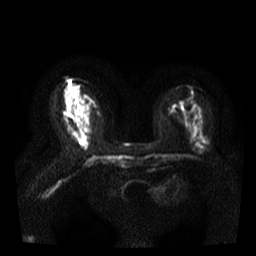
Breast MRI, one axial slice. Slice 18 of 40 in the series (ordered by position). Diffusion-weighted series; image 2 of 4 stored at this slice position (different b-values; order by instance number). 3 T. 5 mm slice thickness. 256 × 256 image matrix, field of view 300 × 300 mm. Female patient.
Annotated regions visible in this slice (expert manual segmentation):
- tumour on diffusion-weighted imaging: bounding box [x1, y1, x2, y2] px = [72, 101, 82, 117]